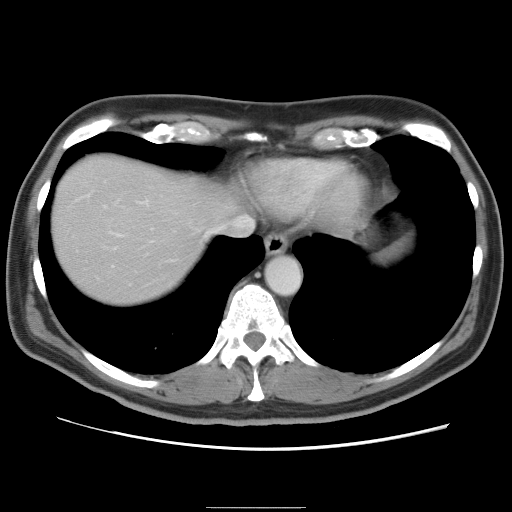
Contrast-enhanced abdominal CT, one axial slice; slice 73 of 87 in the series (ordered by position); 120 kVp; soft-tissue window (W 400 / L 40 HU); 512 × 512 image matrix. Male patient, age 63 years. From the clinical record (not read from this slice): diagnosis: colorectal cancer liver metastases, imaged before liver resection; multiple liver metastases: no; largest metastasis: 9 cm.
Outlined on this slice (manually delineated by an expert):
- hepatic veins: bounding box [x1, y1, x2, y2] px = [105, 181, 253, 244]
- liver: [49, 154, 236, 307]
- planned liver remnant (the part of the liver to remain after resection): [50, 172, 204, 306]
- portal vein (with intrahepatic branches): [102, 196, 155, 285]